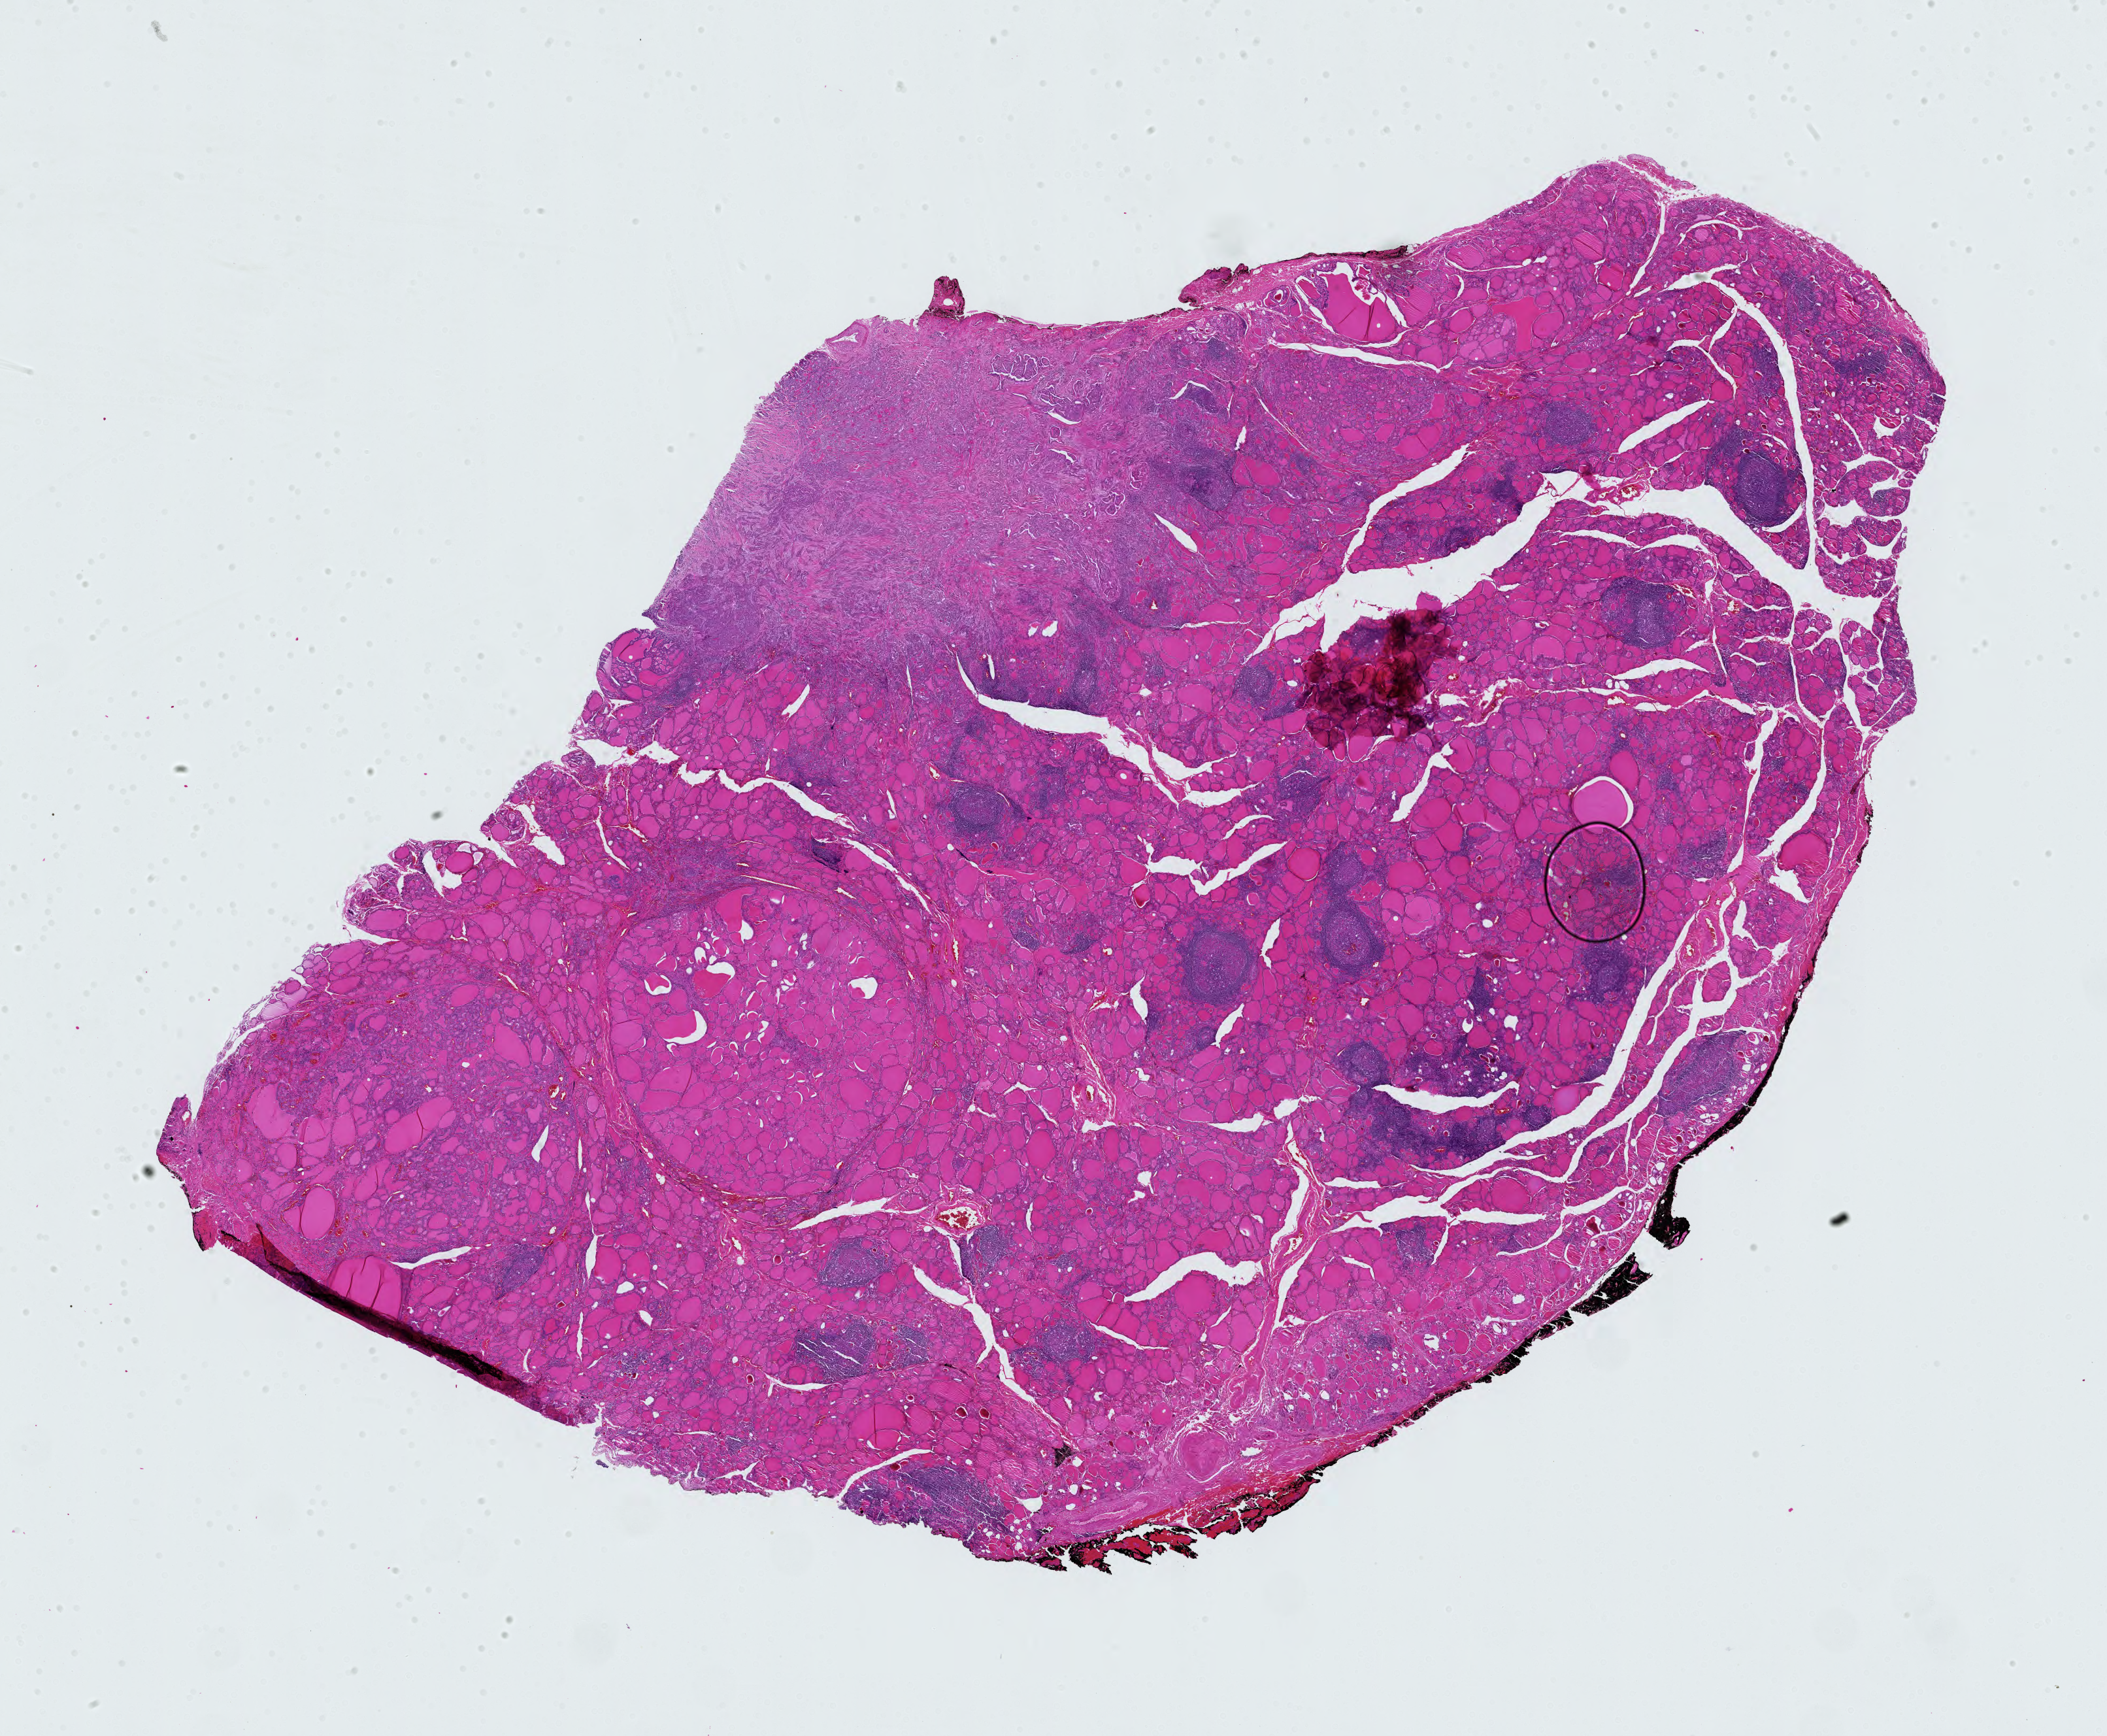
H&E whole-slide image, shown as a low-resolution overview of the whole scanned area (about 23.4 x 19.3 mm, acquisition: 40x scan). Formalin-fixed paraffin-embedded (FFPE) diagnostic section. Thyroid, primary tumour sample. Female, age 50 years at initial diagnosis.
Diagnosis: Papillary adenocarcinoma, NOS (thyroid gland).